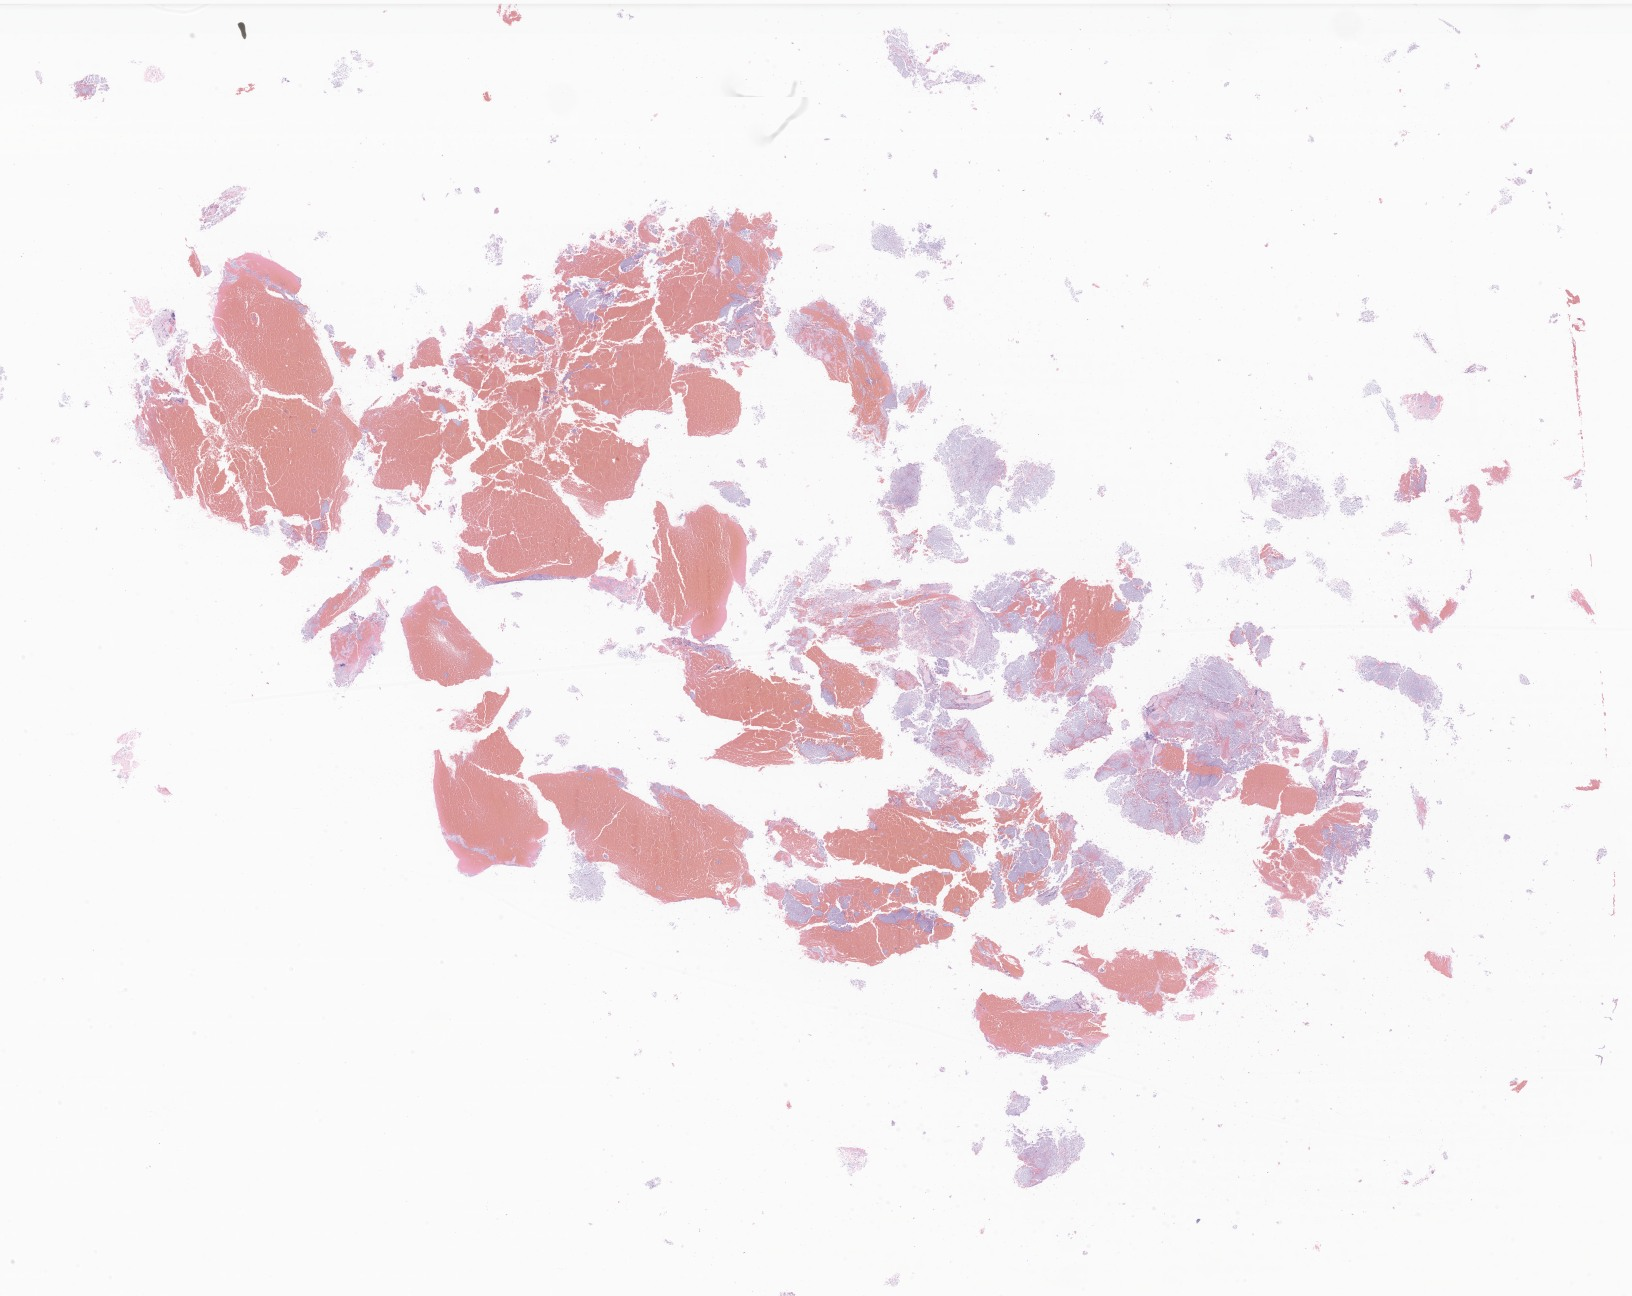
Whole-slide image, haematoxylin and eosin stain of tumor tissue from the occipital lobe — low-resolution overview of the scanned area, about 27.5 x 21.9 mm. Formalin-fixed paraffin-embedded section. Patient: female, age 74 months.
Recorded diagnosis: Medulloblastoma, NOS.